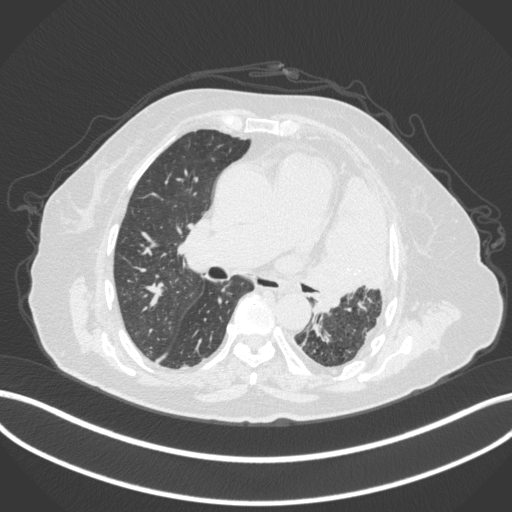
Chest CT, one axial slice; slice 212 of 399 in the series (ordered by position); 120 kVp; lung window (W 1500 / L -600 HU); 1 mm slice thickness; 512 × 512 image matrix. Patient: female, 75 years. Case-level facts recorded for this patient, not image findings: clinical TNM (as recorded): T3 N3 M1.
Outlined on this slice (bounding box drawn by a radiologist):
- lung tumour (recorded histology: adenocarcinoma): bounding box <305,176,387,318> (left, top, right, bottom; pixels)